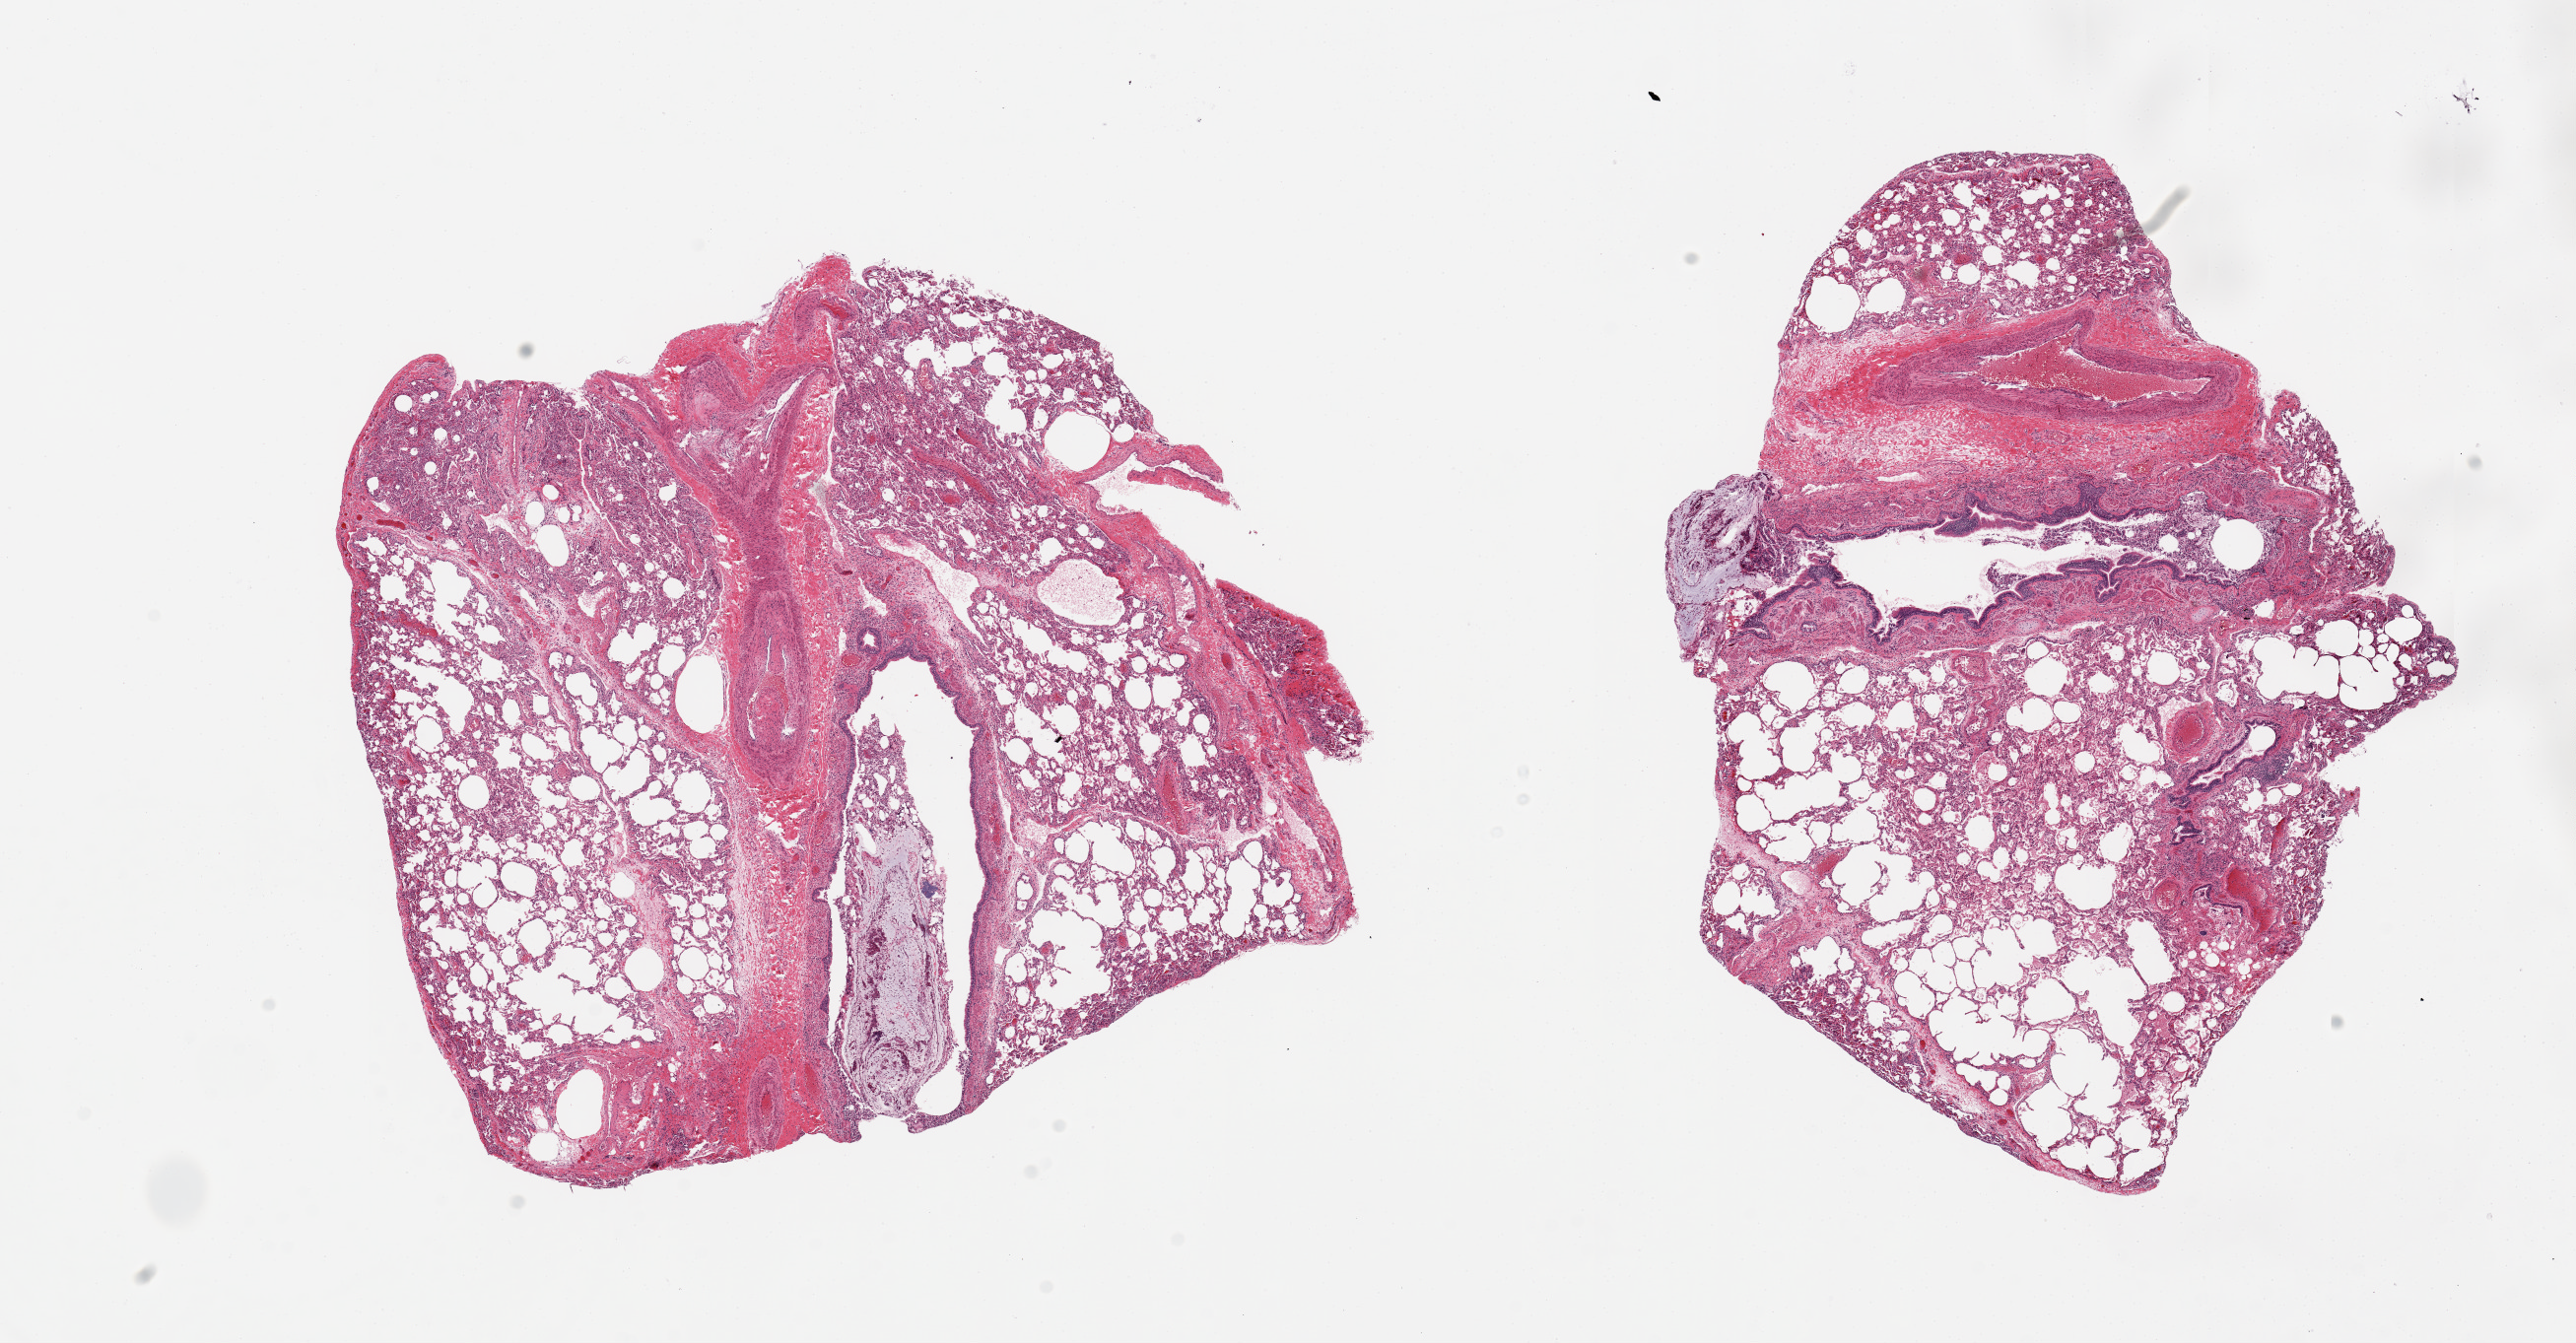
Whole-slide image, hematoxylin and eosin (H&E) stain, a low-resolution overview of the entire scanned area, about 20.7 x 10.8 mm, PAXgene-fixed paraffin-embedded (PFPE) section, target tissue: lung, tissue donor sample. Donor: male.
• review note (as recorded): 2 pieces, 8x7 & 8x6mm; mild congestion